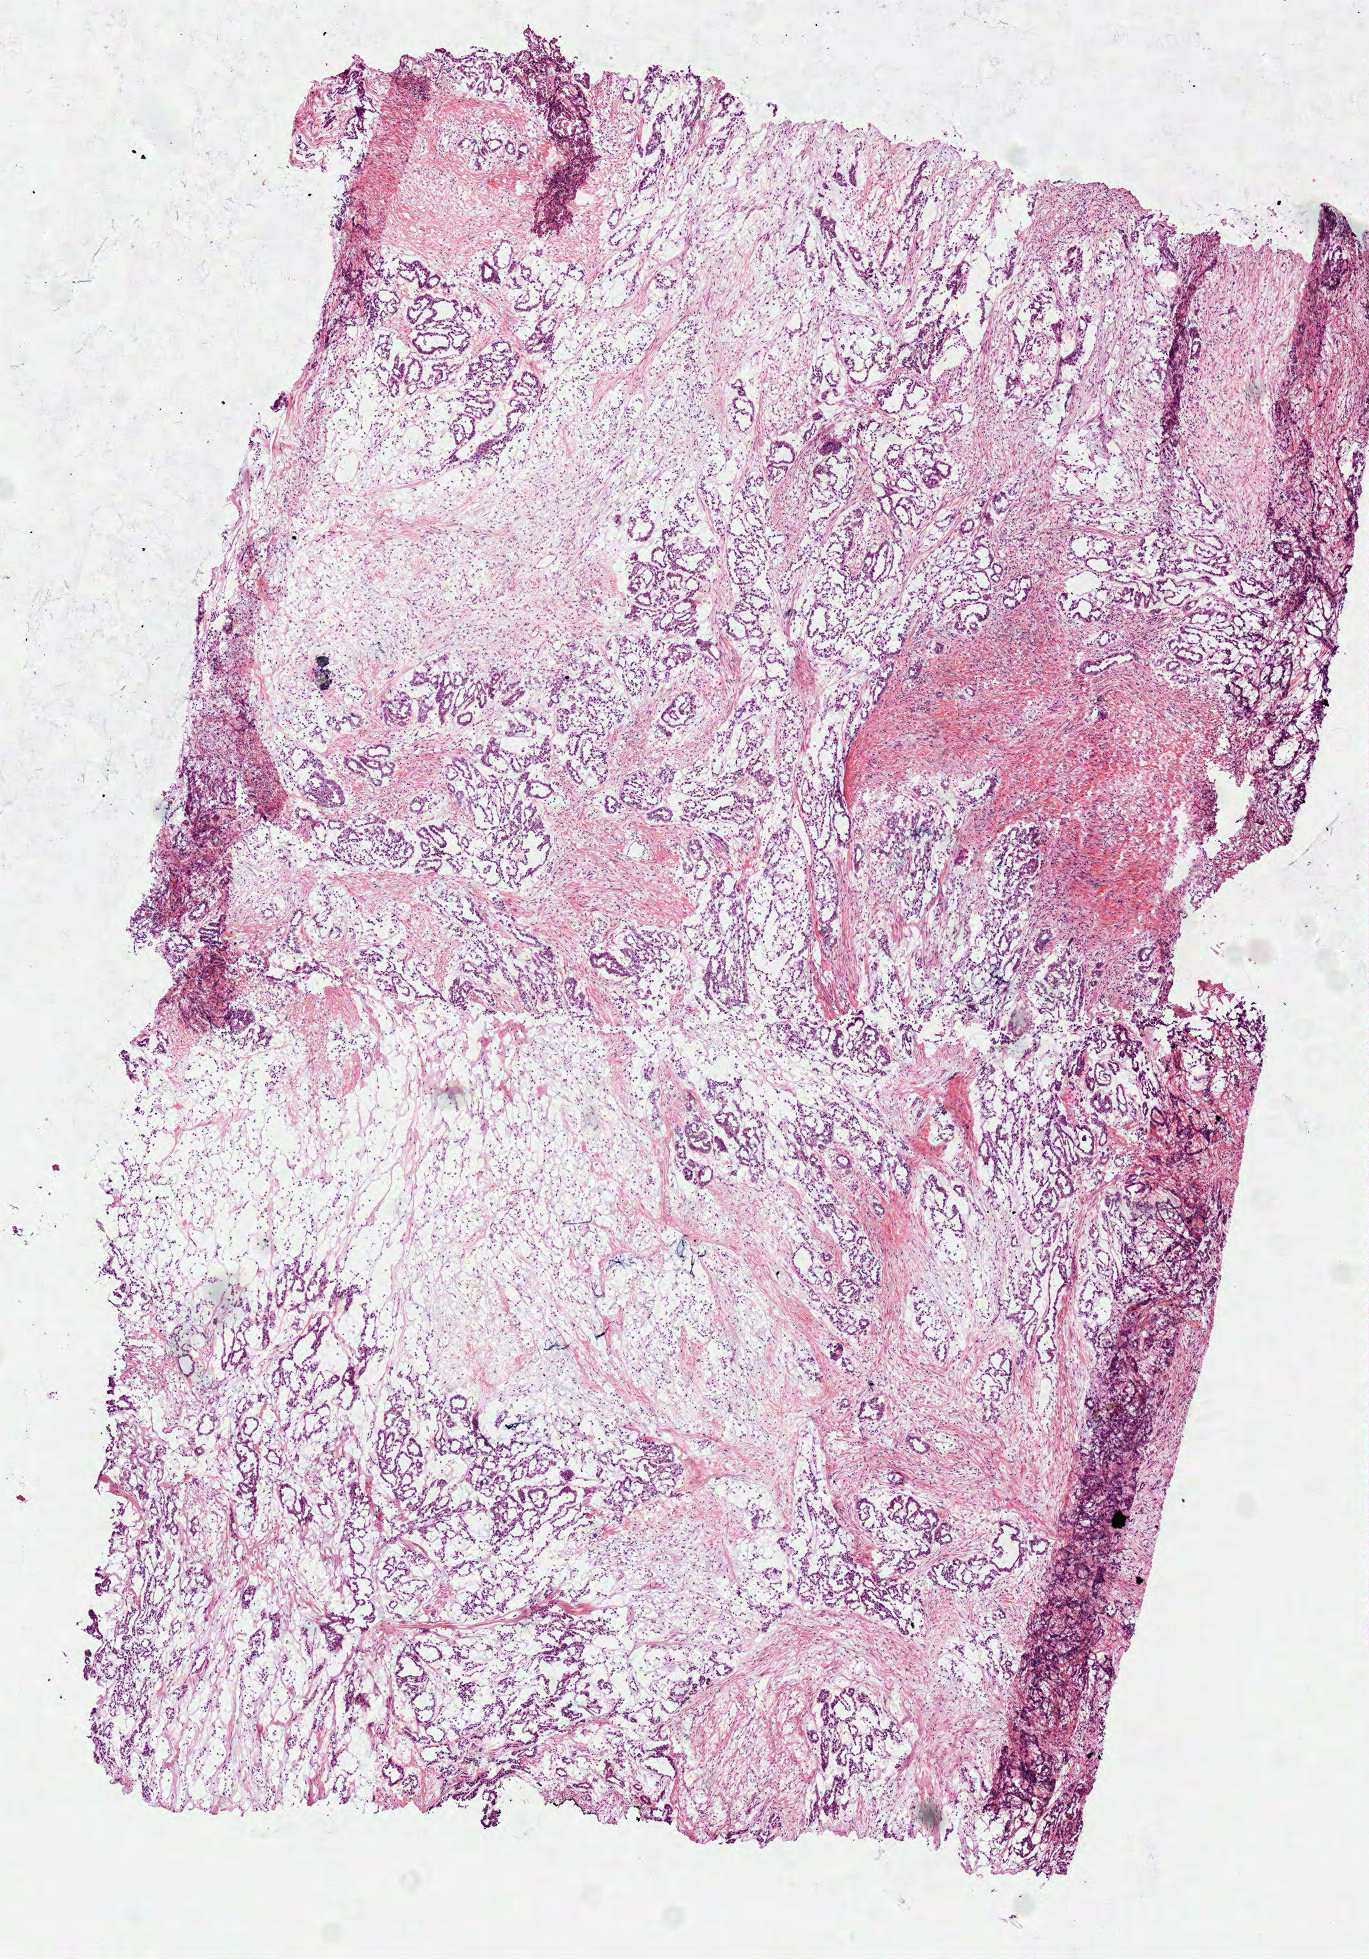
H&E-stained whole-slide image — whole scanned area (about 5.4 x 7.7 mm) shown as a low-resolution overview. Frozen section from the top of the tissue portion. Kidney, primary tumour sample. Female patient; age at initial diagnosis 53 years. Composition of this section per pathologist review: tumour cells 75%, tumour nuclei 80%, normal cells 0%, stromal cells 25%, necrosis 0%.
Lymph nodes positive (case pathology): 4 of 4 examined. AJCC pathologic stage: IV (6th edition). Pathologic diagnosis: Papillary adenocarcinoma, NOS.